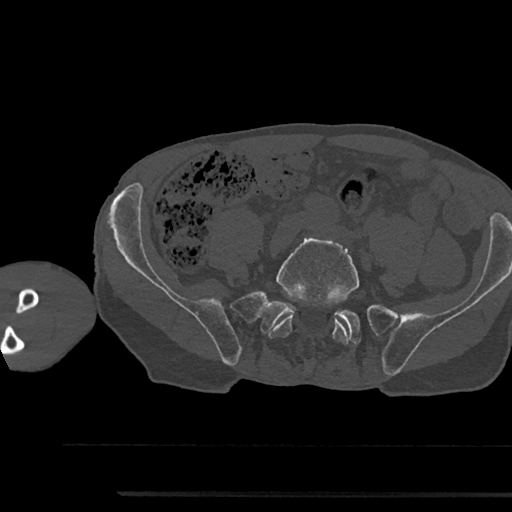
CT including the spine, one axial slice. Slice 327 of 797 in the series (ordered by position). 120 kVp. Bone window (W 1800 / L 400 HU). 512 × 512 image matrix. Patient: male, 79 years. Case-level facts recorded for this patient, not image findings: primary cancer: prostate.
Annotated regions visible in this slice (semi-automatically segmented with operator editing):
- L5 vertebra: box from (x=267, y=238) to (x=359, y=344) px